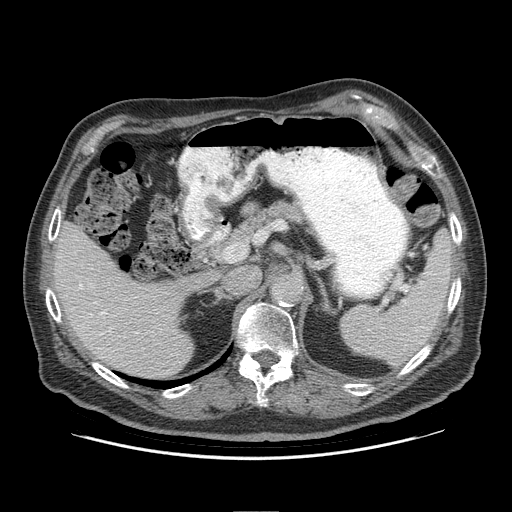
Contrast-enhanced abdominal CT (liver protocol), one axial slice; slice 56 of 95 in the series (ordered by position); reconstruction kernel STANDARD; 140 kVp; soft-tissue window (W 400 / L 40 HU); 2.5 mm slice thickness; 512 × 512 image matrix, field of view 400 × 400 mm. Case-level facts recorded for this patient, not image findings: diagnosis: hepatocellular carcinoma (patient treated with transarterial chemoembolisation; whether this scan precedes or follows treatment is not stated here); TNM stage (as recorded): Stage-IVB; Child-Pugh class: A; tumour differentiation: well differentiated.
Annotated regions visible in this slice (semi-automatically segmented with operator editing):
- liver parenchyma outside the tumour (the mass and vessels are separate outlines, so this box may not span the whole liver): bounding box <54,222,214,378> (left, top, right, bottom; pixels)
- liver vessels: <80,285,138,335>